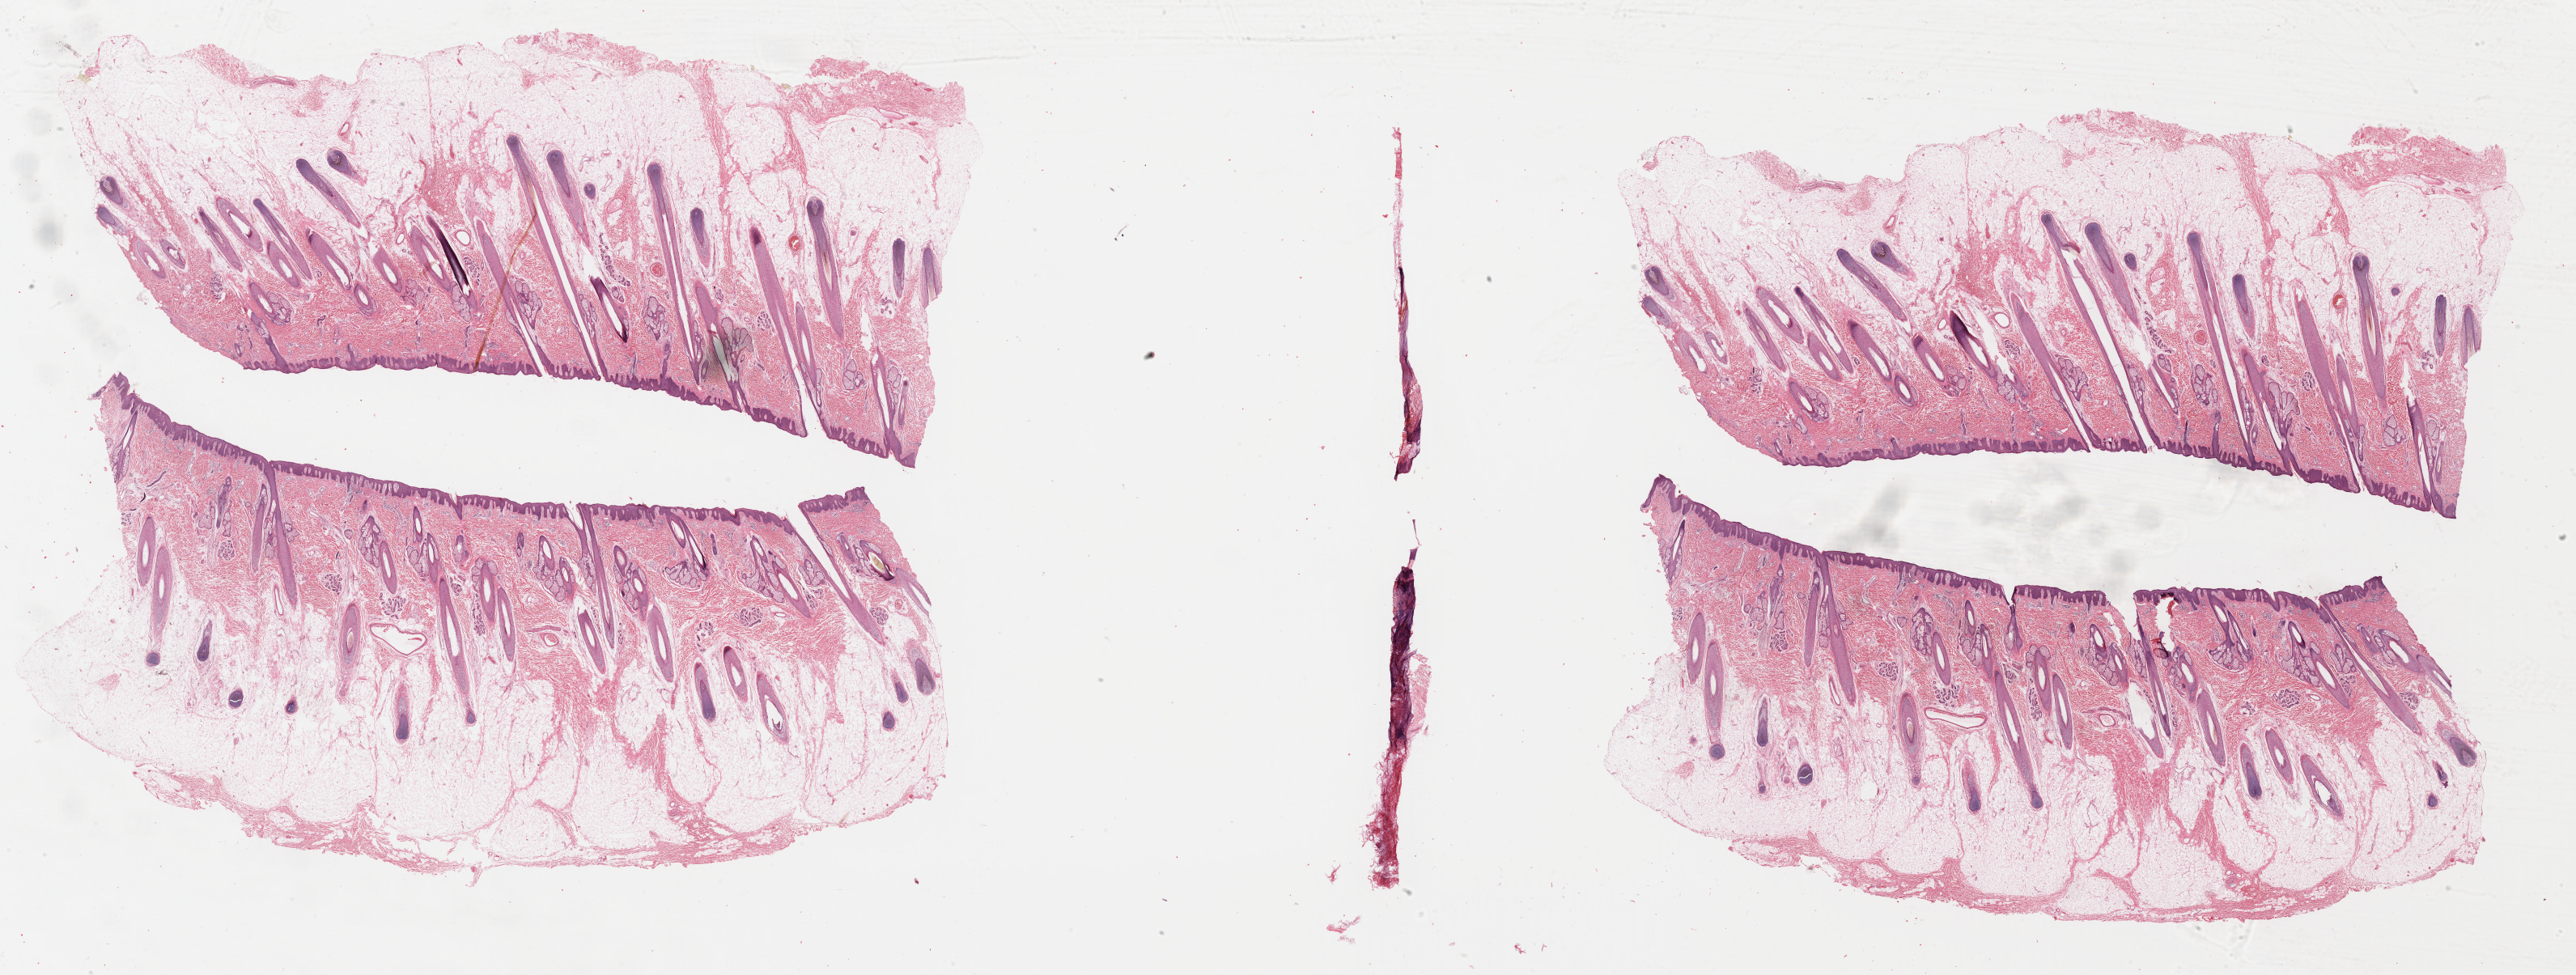
Whole-slide histology image, H&E-stained, a low-resolution overview of the entire scanned area, about 50.0 x 18.9 mm; FFPE section; metastatic tumour sample, sampled site not recorded. Male, age 19 years at initial diagnosis.
This section: metastatic tumour tissue. Patient diagnosis: Malignant melanoma, NOS.